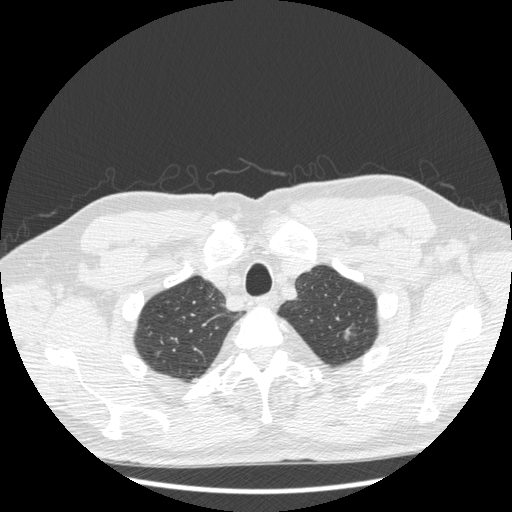
Low-dose screening chest CT, one axial slice; slice 192 of 223 in the series (ordered by position); reconstruction kernel STANDARD; lung window (W 1500 / L -600 HU); 512 × 512 image matrix.
Outlined on this slice (expert manual segmentation):
- lesion 1 (tumor, upper lobe of left lung): box from (x=344, y=327) to (x=352, y=340) px